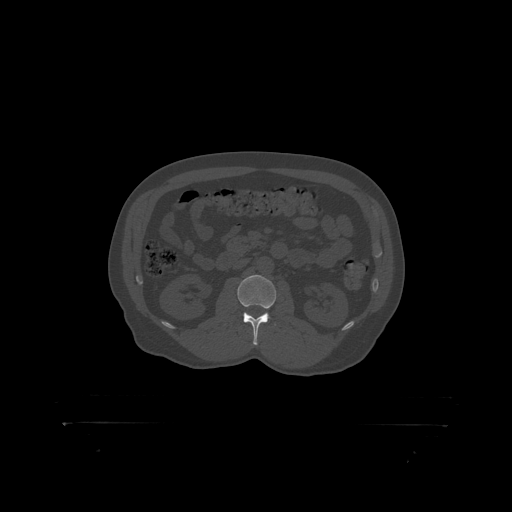
CT including the spine, one axial slice; position 292 of 399 along the scan axis; reconstruction kernel STANDARD; 120 kVp; bone window (W 1800 / L 400 HU); 1.25 mm slice thickness; 512 × 512 image matrix, field of view 650 × 650 mm. Male patient, age 46 years. From the clinical record (not read from this slice): primary cancer: skin.
Structures marked on this image (semi-automatically segmented with operator editing):
- L2 vertebra: bounding box (x1, y1, x2, y2) in pixels: (238, 276, 277, 319)